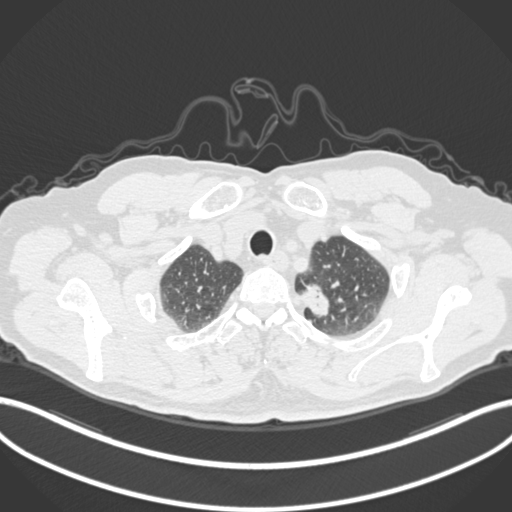
Chest CT, one axial slice. Position 283 of 306 along the scan axis. Reconstruction kernel B30f. 120 kVp. Lung window (W 1500 / L -600 HU). 1 mm slice thickness. 512 × 512 image matrix. Patient: male, 64 years. Case-level facts recorded for this patient, not image findings: clinical TNM (as recorded): T1c N0 M0.
Outlined on this slice (rectangle marked by the reading radiologist):
- lung tumour (recorded histology: adenocarcinoma): bounding box <299,282,332,319> (left, top, right, bottom; pixels)